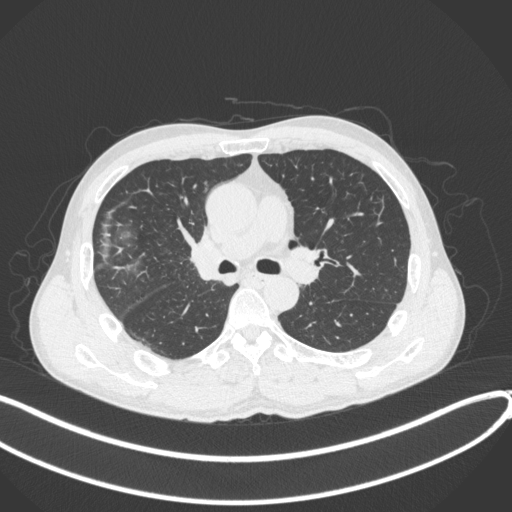
Chest CT, one axial slice; position 234 of 409 along the scan axis; reconstruction kernel B31f; 120 kVp; lung window (W 1500 / L -600 HU); 1 mm slice thickness; 512 × 512 image matrix, field of view 400 × 400 mm. Male patient, age 53 years. Case-level facts recorded for this patient, not image findings: clinical TNM (as recorded): T1b N0 M0.
Outlined on this slice (bounding box drawn by a radiologist):
- lung tumour (recorded histology: squamous cell carcinoma): bounding box [x1, y1, x2, y2] px = [180, 220, 222, 283]